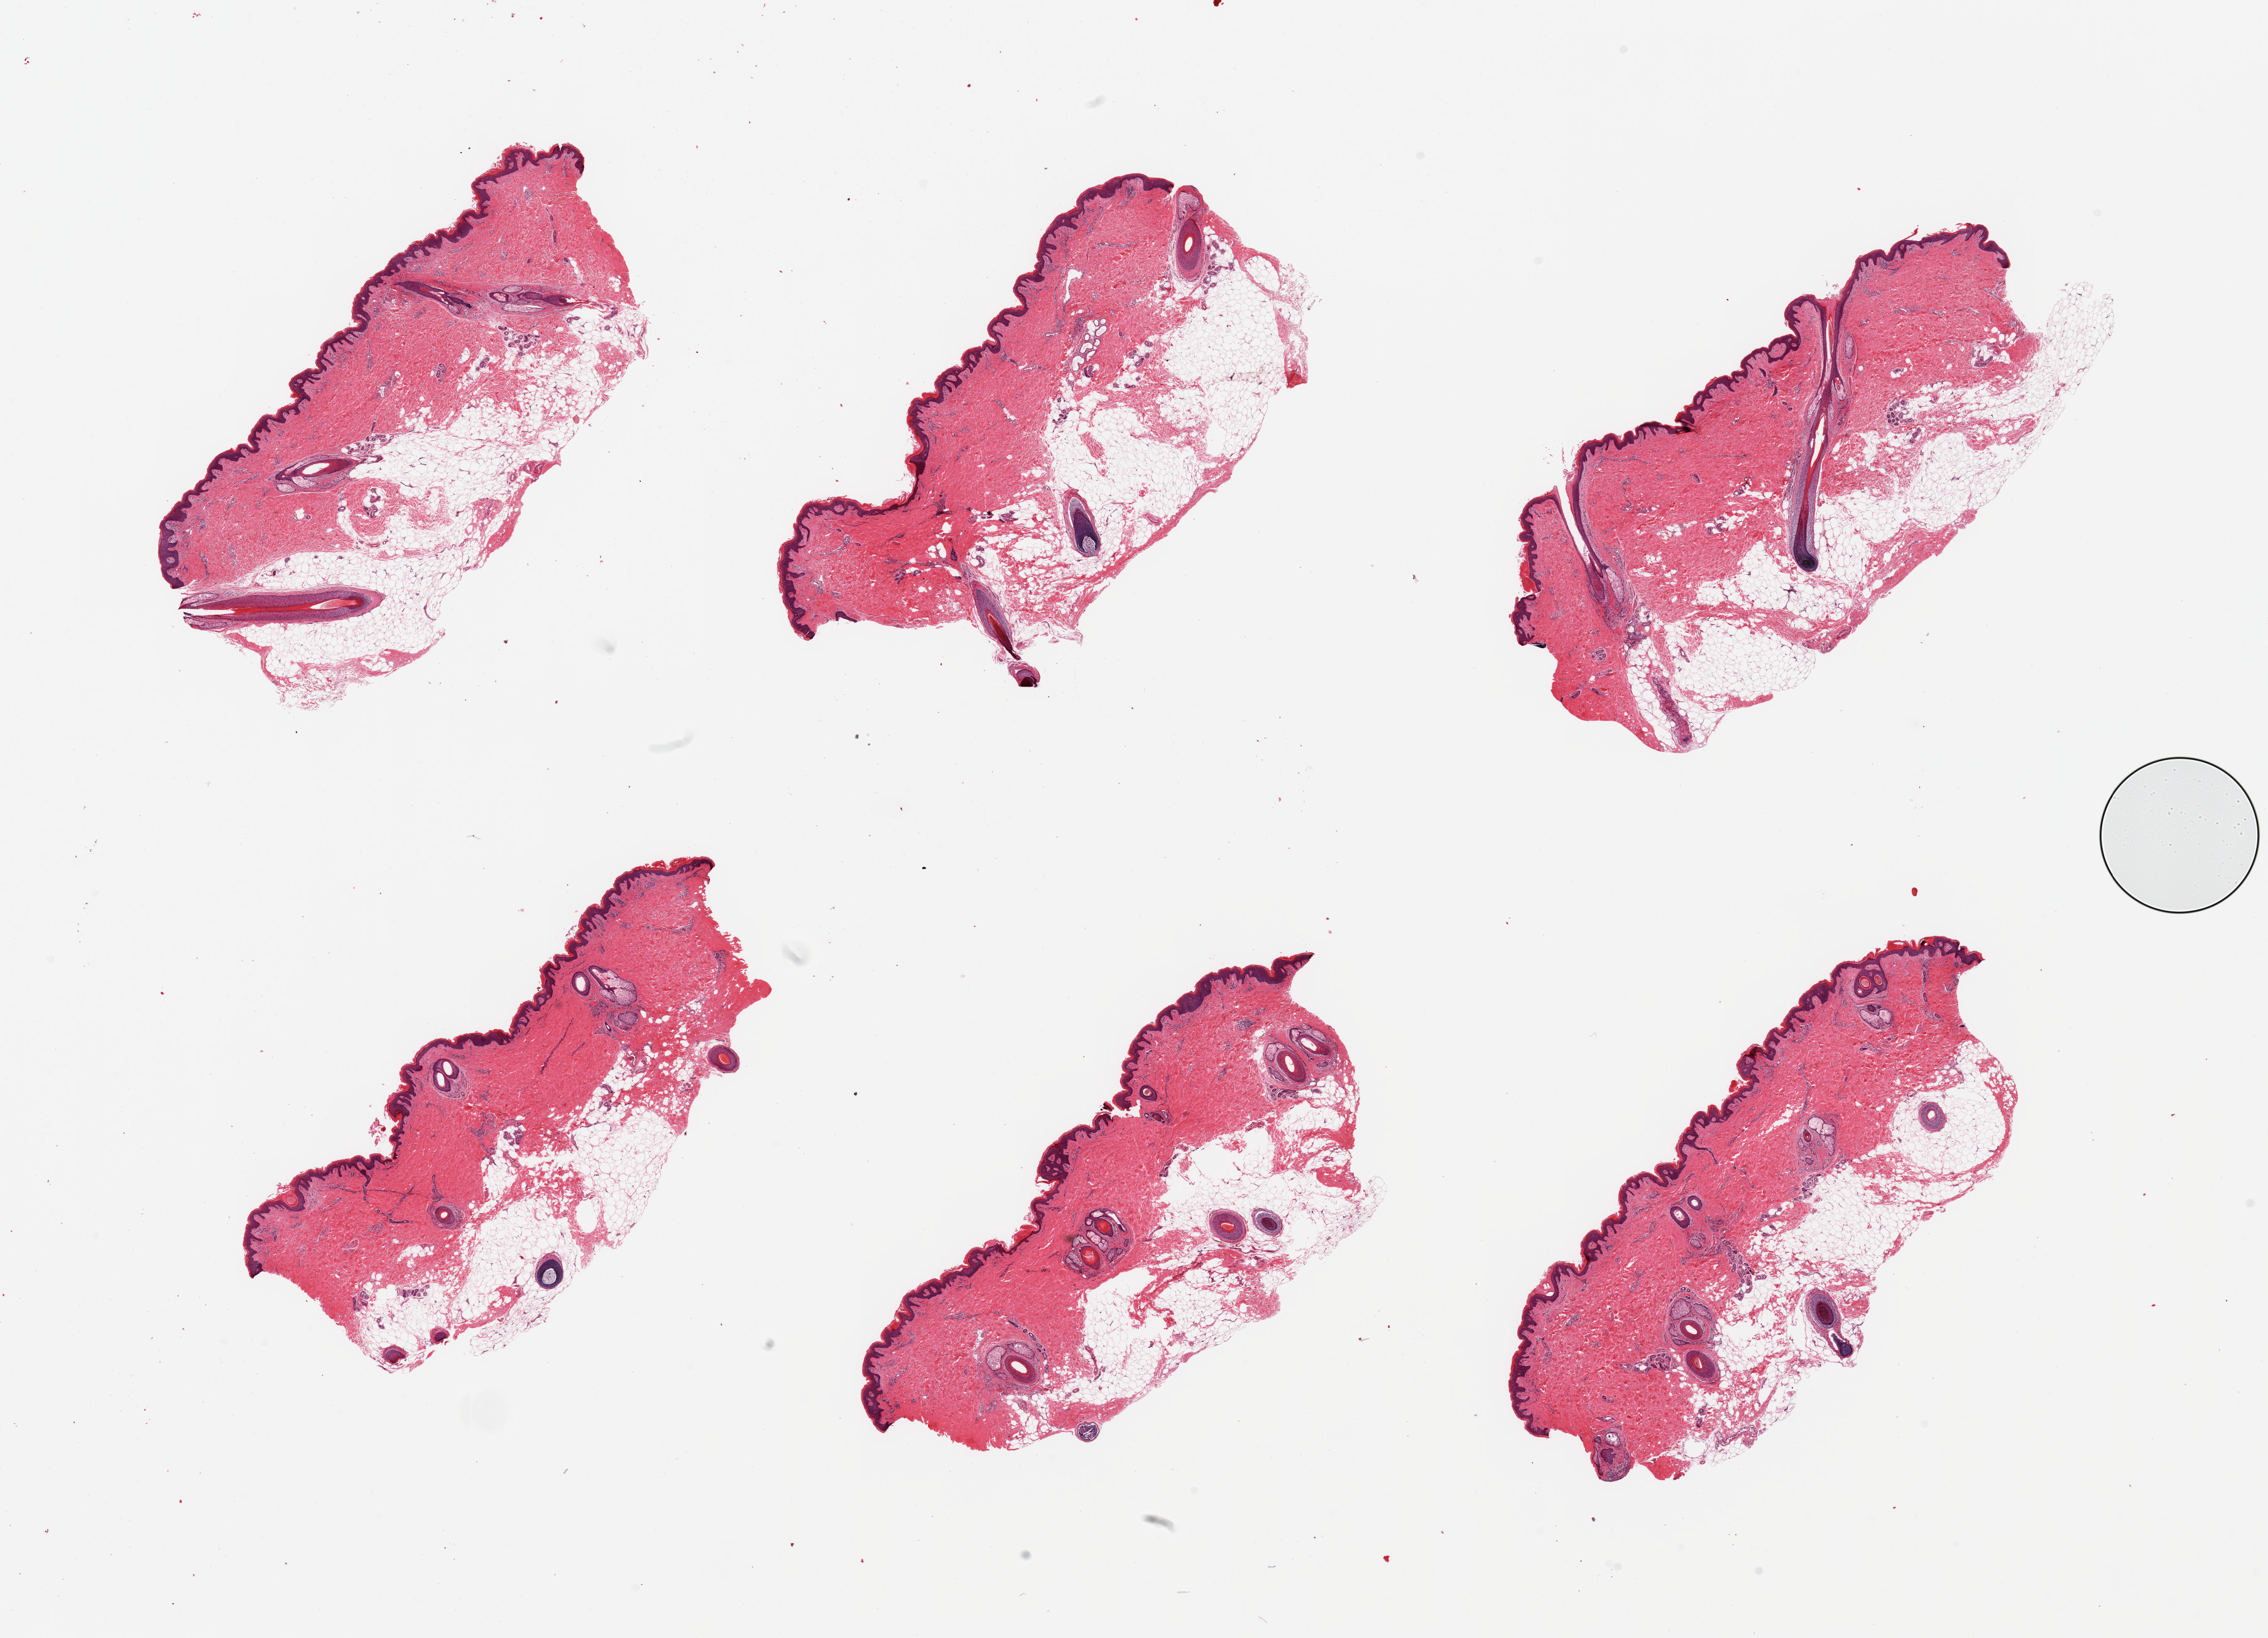
H&E whole-slide image, brightfield — low-resolution overview of the scanned area, about 28.5 x 20.6 mm (slide scanned at 20x), PAXgene-fixed, paraffin-embedded tissue, sampled site (target tissue): skin of suprapubic region, tissue donor sample. Donor sex: male.
• review note (as recorded): 6 pieces; hair bearing skin with up to 50% external fat